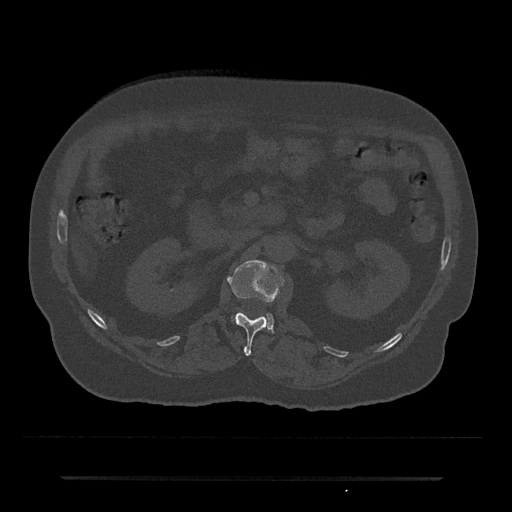
CT including the spine, one axial slice; position 54 of 797 along the scan axis; reconstruction kernel Br40s/3; 120 kVp; bone window (W 1800 / L 400 HU); 0.5 mm slice thickness; 512 × 512 image matrix. Patient: male, 69 years. From the clinical record (not read from this slice): primary cancer: prostate.
Outlined on this slice (semi-automatically segmented with operator editing):
- L1 vertebra: bounding box (x1, y1, x2, y2) in pixels: (227, 260, 284, 355)
- L2 vertebra: (264, 313, 274, 330)